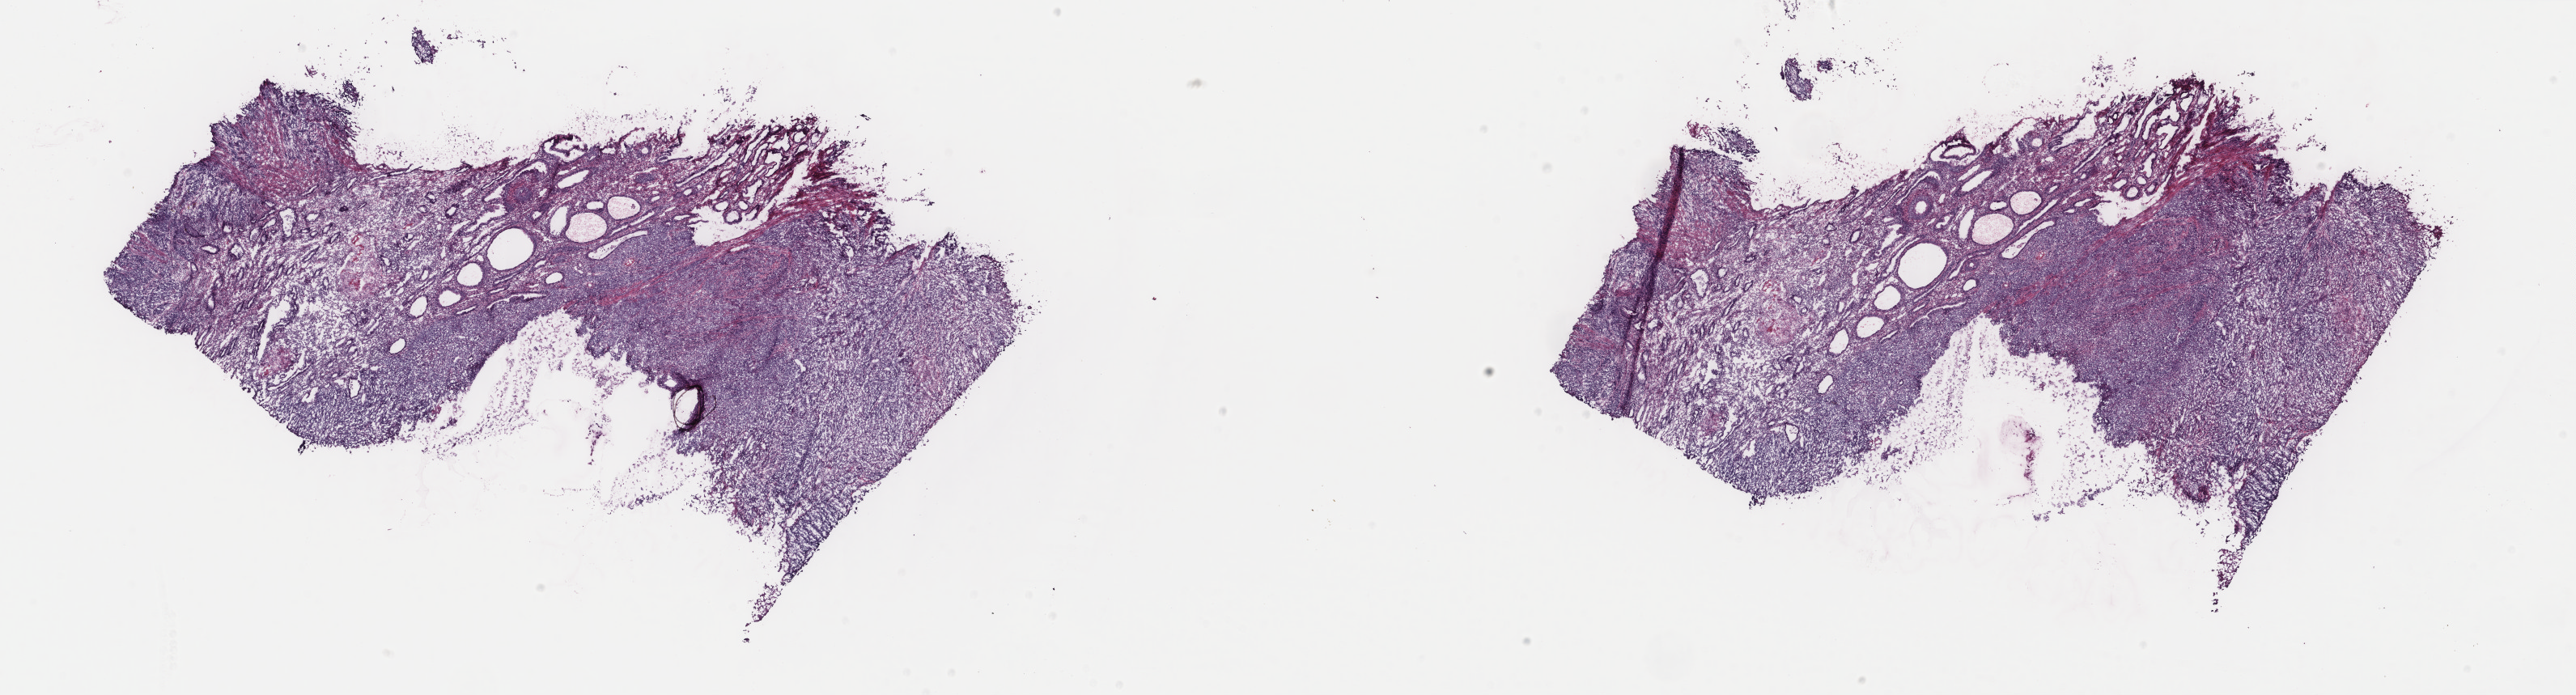
H&E whole-slide image, shown as a low-resolution overview of the whole scanned area (about 25.3 x 6.8 mm). Frozen section from the top of the tissue portion. Primary tumour sample from the uterus. Female patient; age at initial diagnosis 47 years. Histologic grade: G3 (poorly differentiated). Pathologist review of this section (percent, as recorded): tumour cells 60%, tumour nuclei 70%, normal cells 5%, stromal cells 34%, necrosis 1%. Infiltration values recorded for this section: lymphocyte infiltration 5%, monocyte infiltration 1%, neutrophil infiltration 1%.
FIGO stage: IIIC. Lymph nodes positive (case pathology): 1 of 2 examined. Histologic diagnosis: Endometrioid adenocarcinoma, NOS (endometrium).